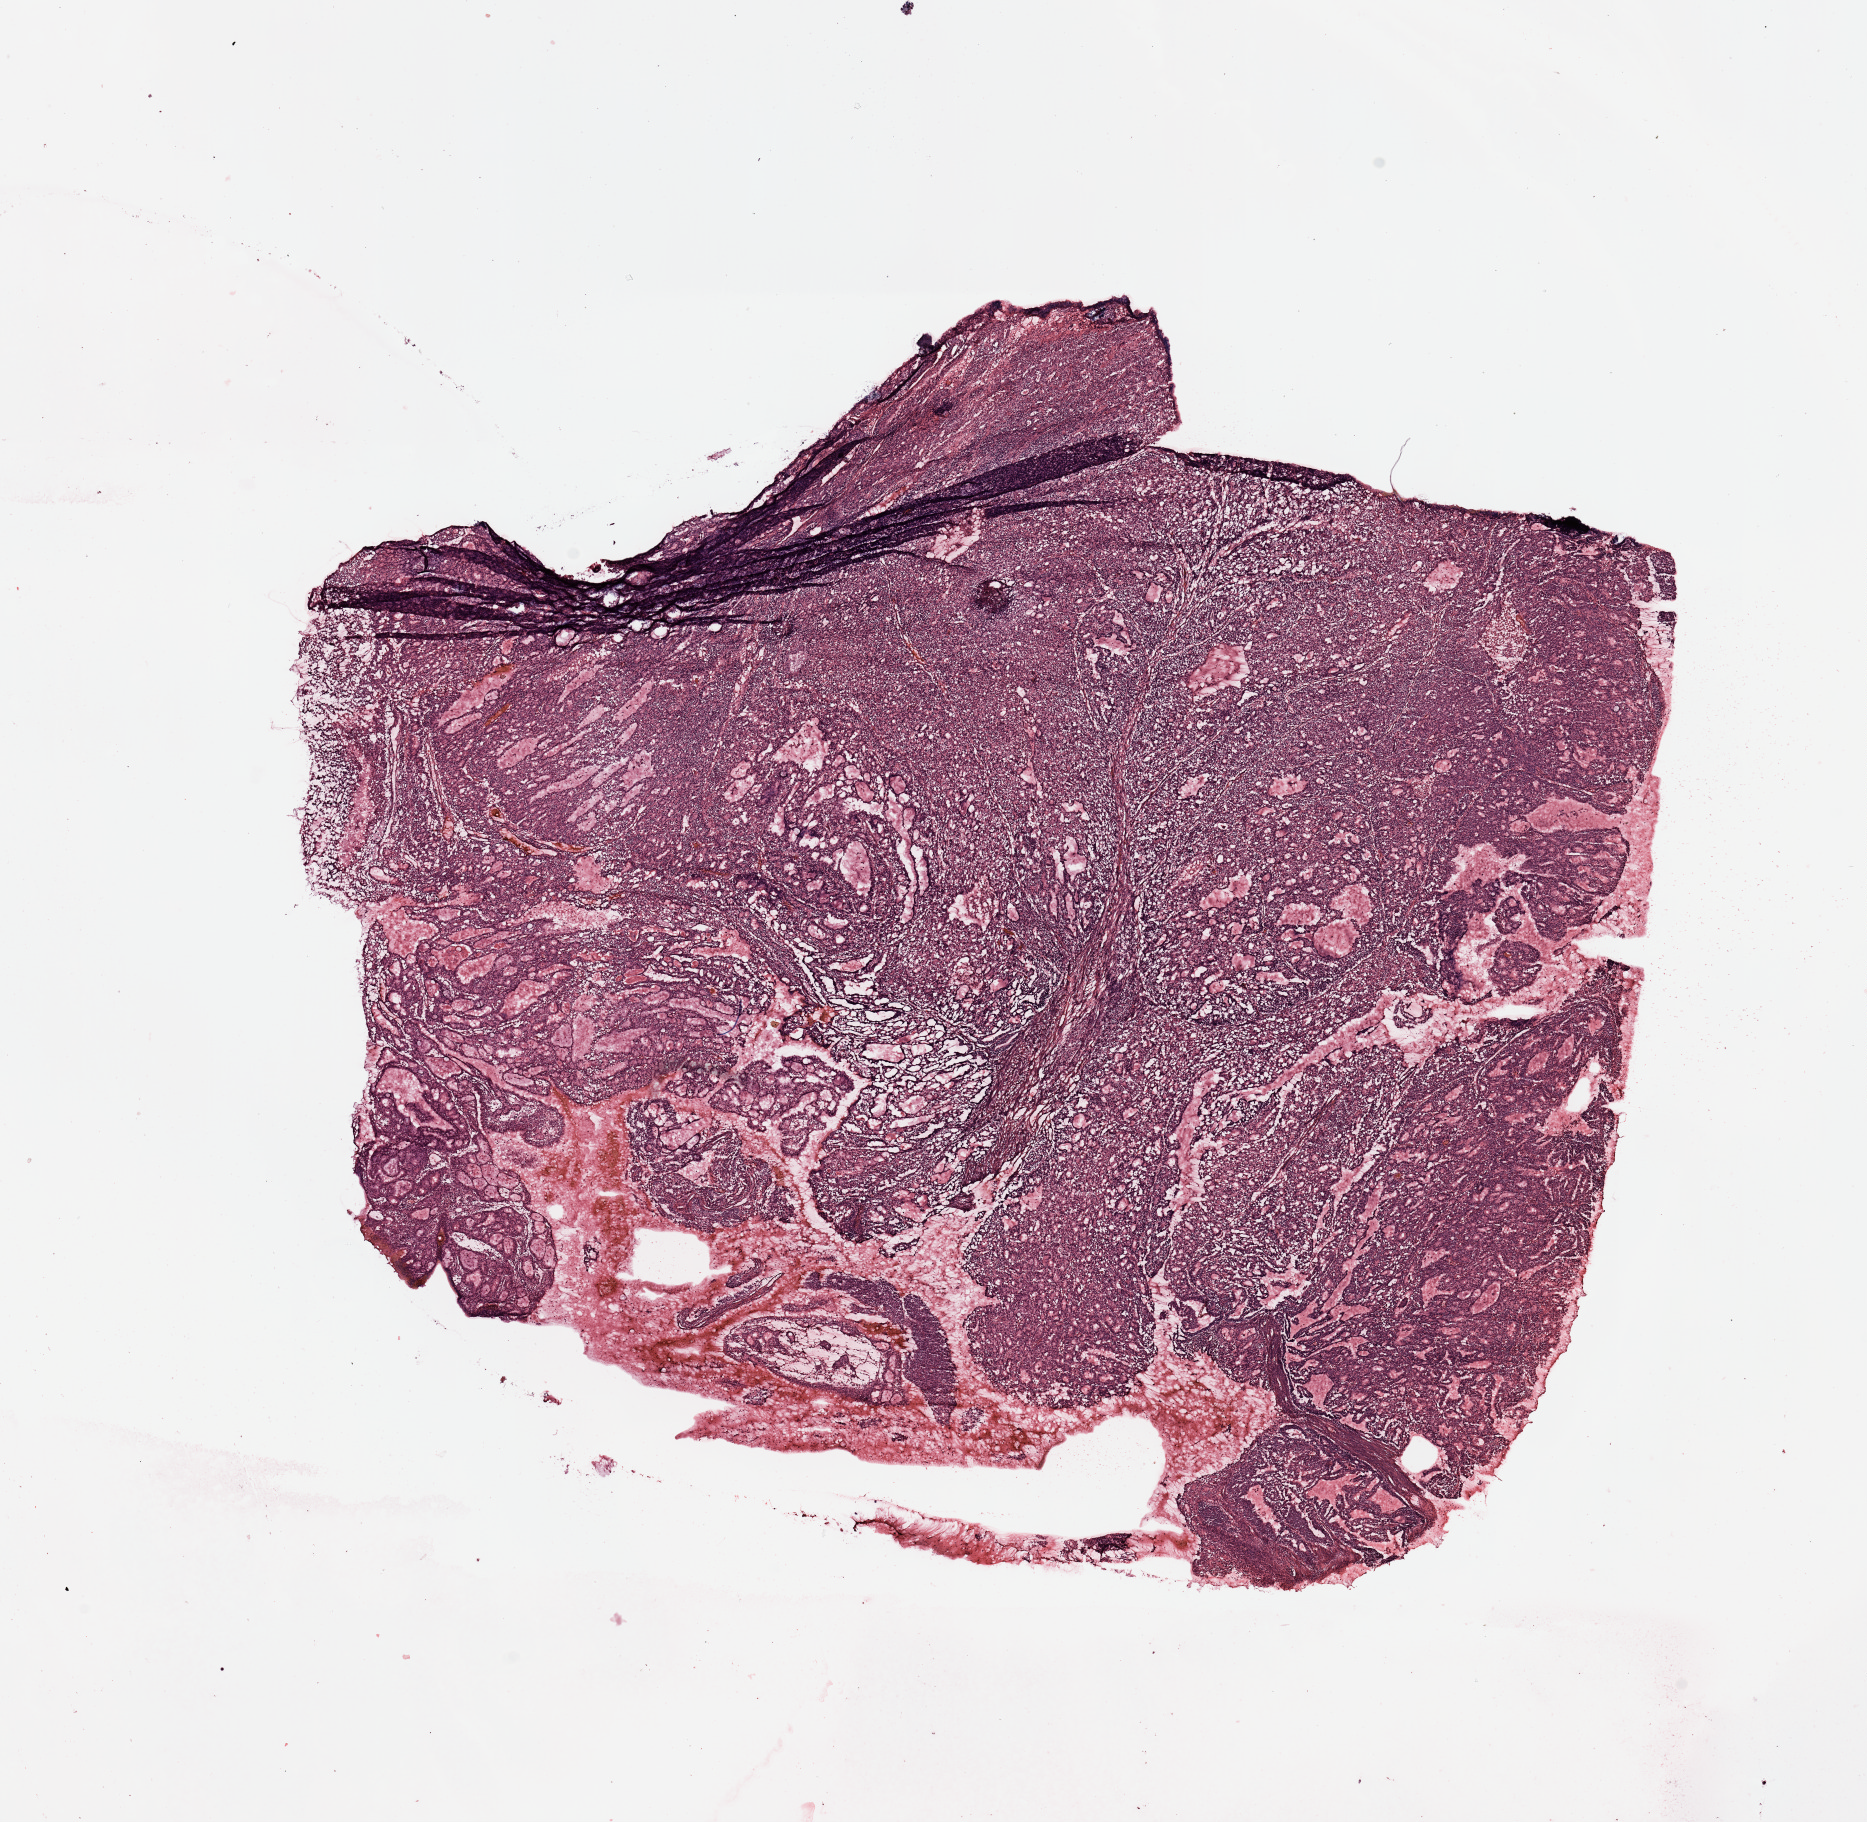
H&E-stained whole-slide image, shown as a low-resolution overview of the whole scanned area (about 14.8 x 14.4 mm, from a 20x scan); tumour tissue sample, uterus. Patient: female, age 67 years. Histologic grade: G2 (moderately differentiated).
AJCC pathologic stage: I. Histologic diagnosis: Endometrioid adenocarcinoma, NOS.